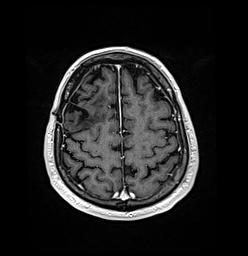
Brain MRI from a brain-tumour surgery series, one axial slice. T1-weighted post-contrast. 1 mm slice thickness. 248 × 256 image matrix, field of view 242 × 250 mm. Case-level facts recorded for this patient, not image findings: histopathology: Oligodendroglioma; WHO grade: 3; IDH mutation: yes; tumour location: Right Frontal.
Structures marked on this image (outlined manually by an expert reader):
- previous resection cavity: box from (x=66, y=92) to (x=89, y=124) px